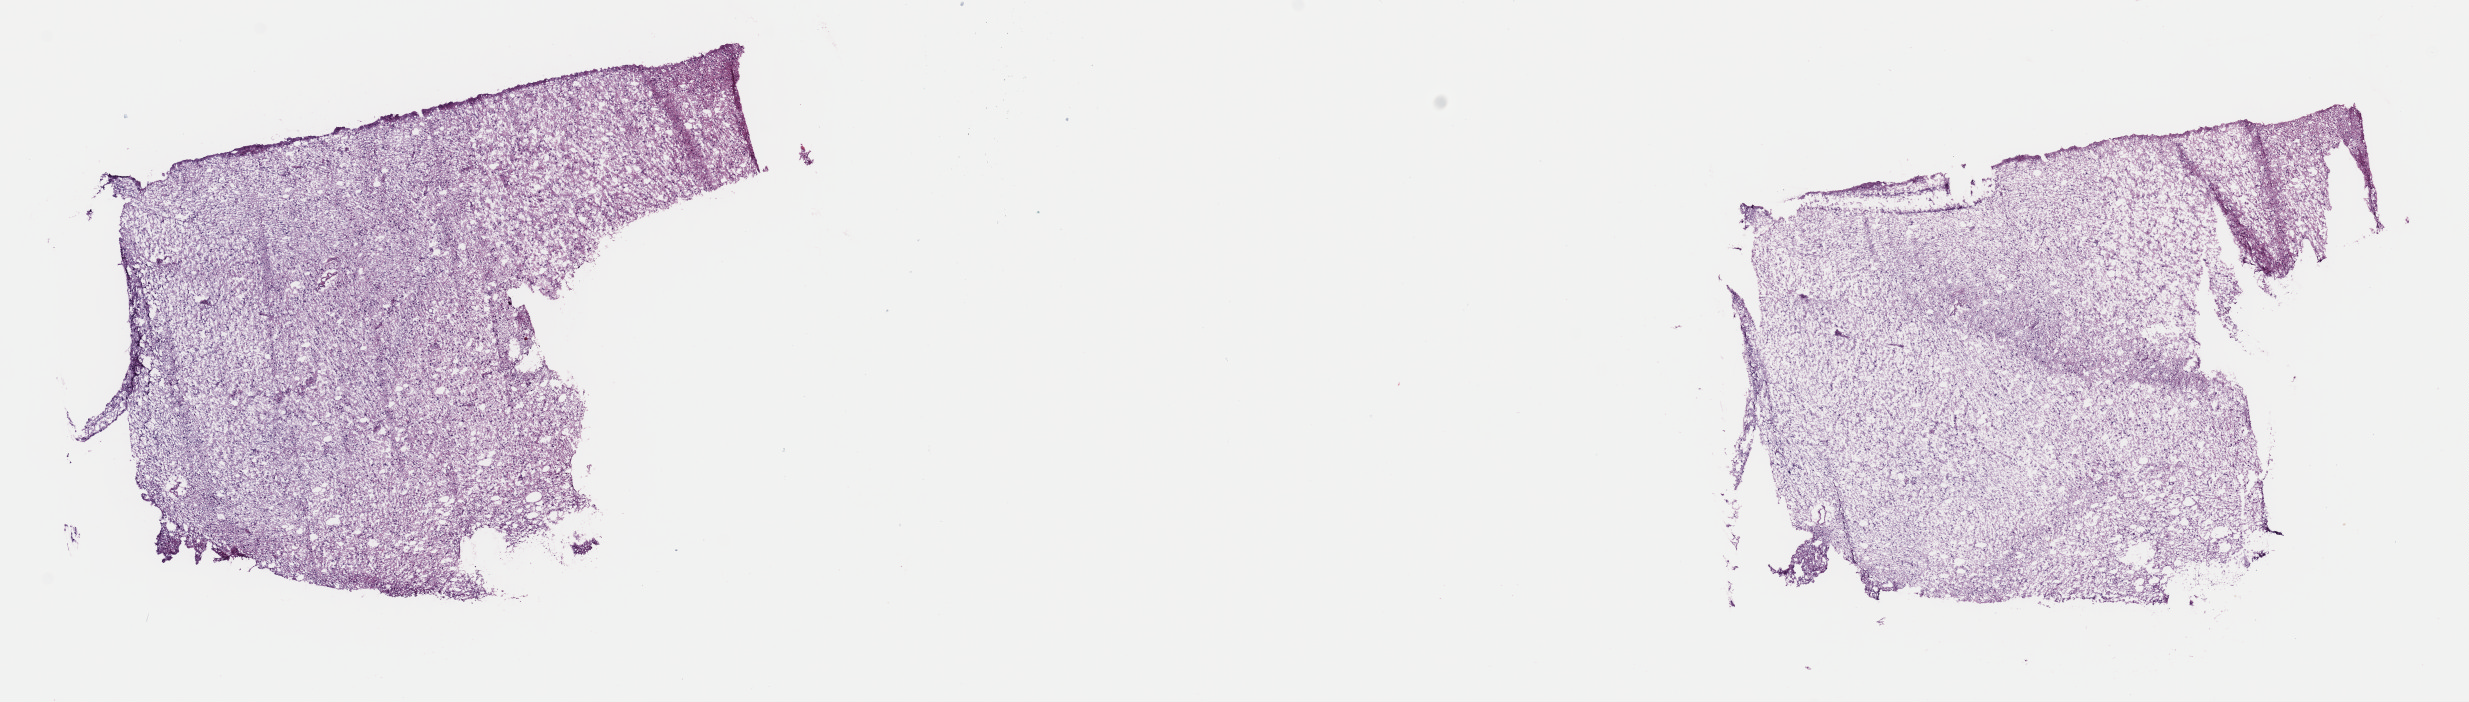
Digitized H&E tissue section (whole slide), shown as a low-resolution overview of the whole scanned area (about 19.5 x 5.5 mm, slide scanned at 40x); frozen section from the top of the tissue portion; primary tumour sample from the brain. Female, age 20 years at initial diagnosis. Histologic grade: G2 (moderately differentiated). Composition of this section per pathologist review: tumour cells 30%, tumour nuclei 70%, normal cells 10%, stromal cells 60%, necrosis 0%. Infiltration values recorded for this section: lymphocyte infiltration 0%, monocyte infiltration 0%, neutrophil infiltration 0%.
Histologic diagnosis: Oligodendroglioma, NOS (cerebrum).